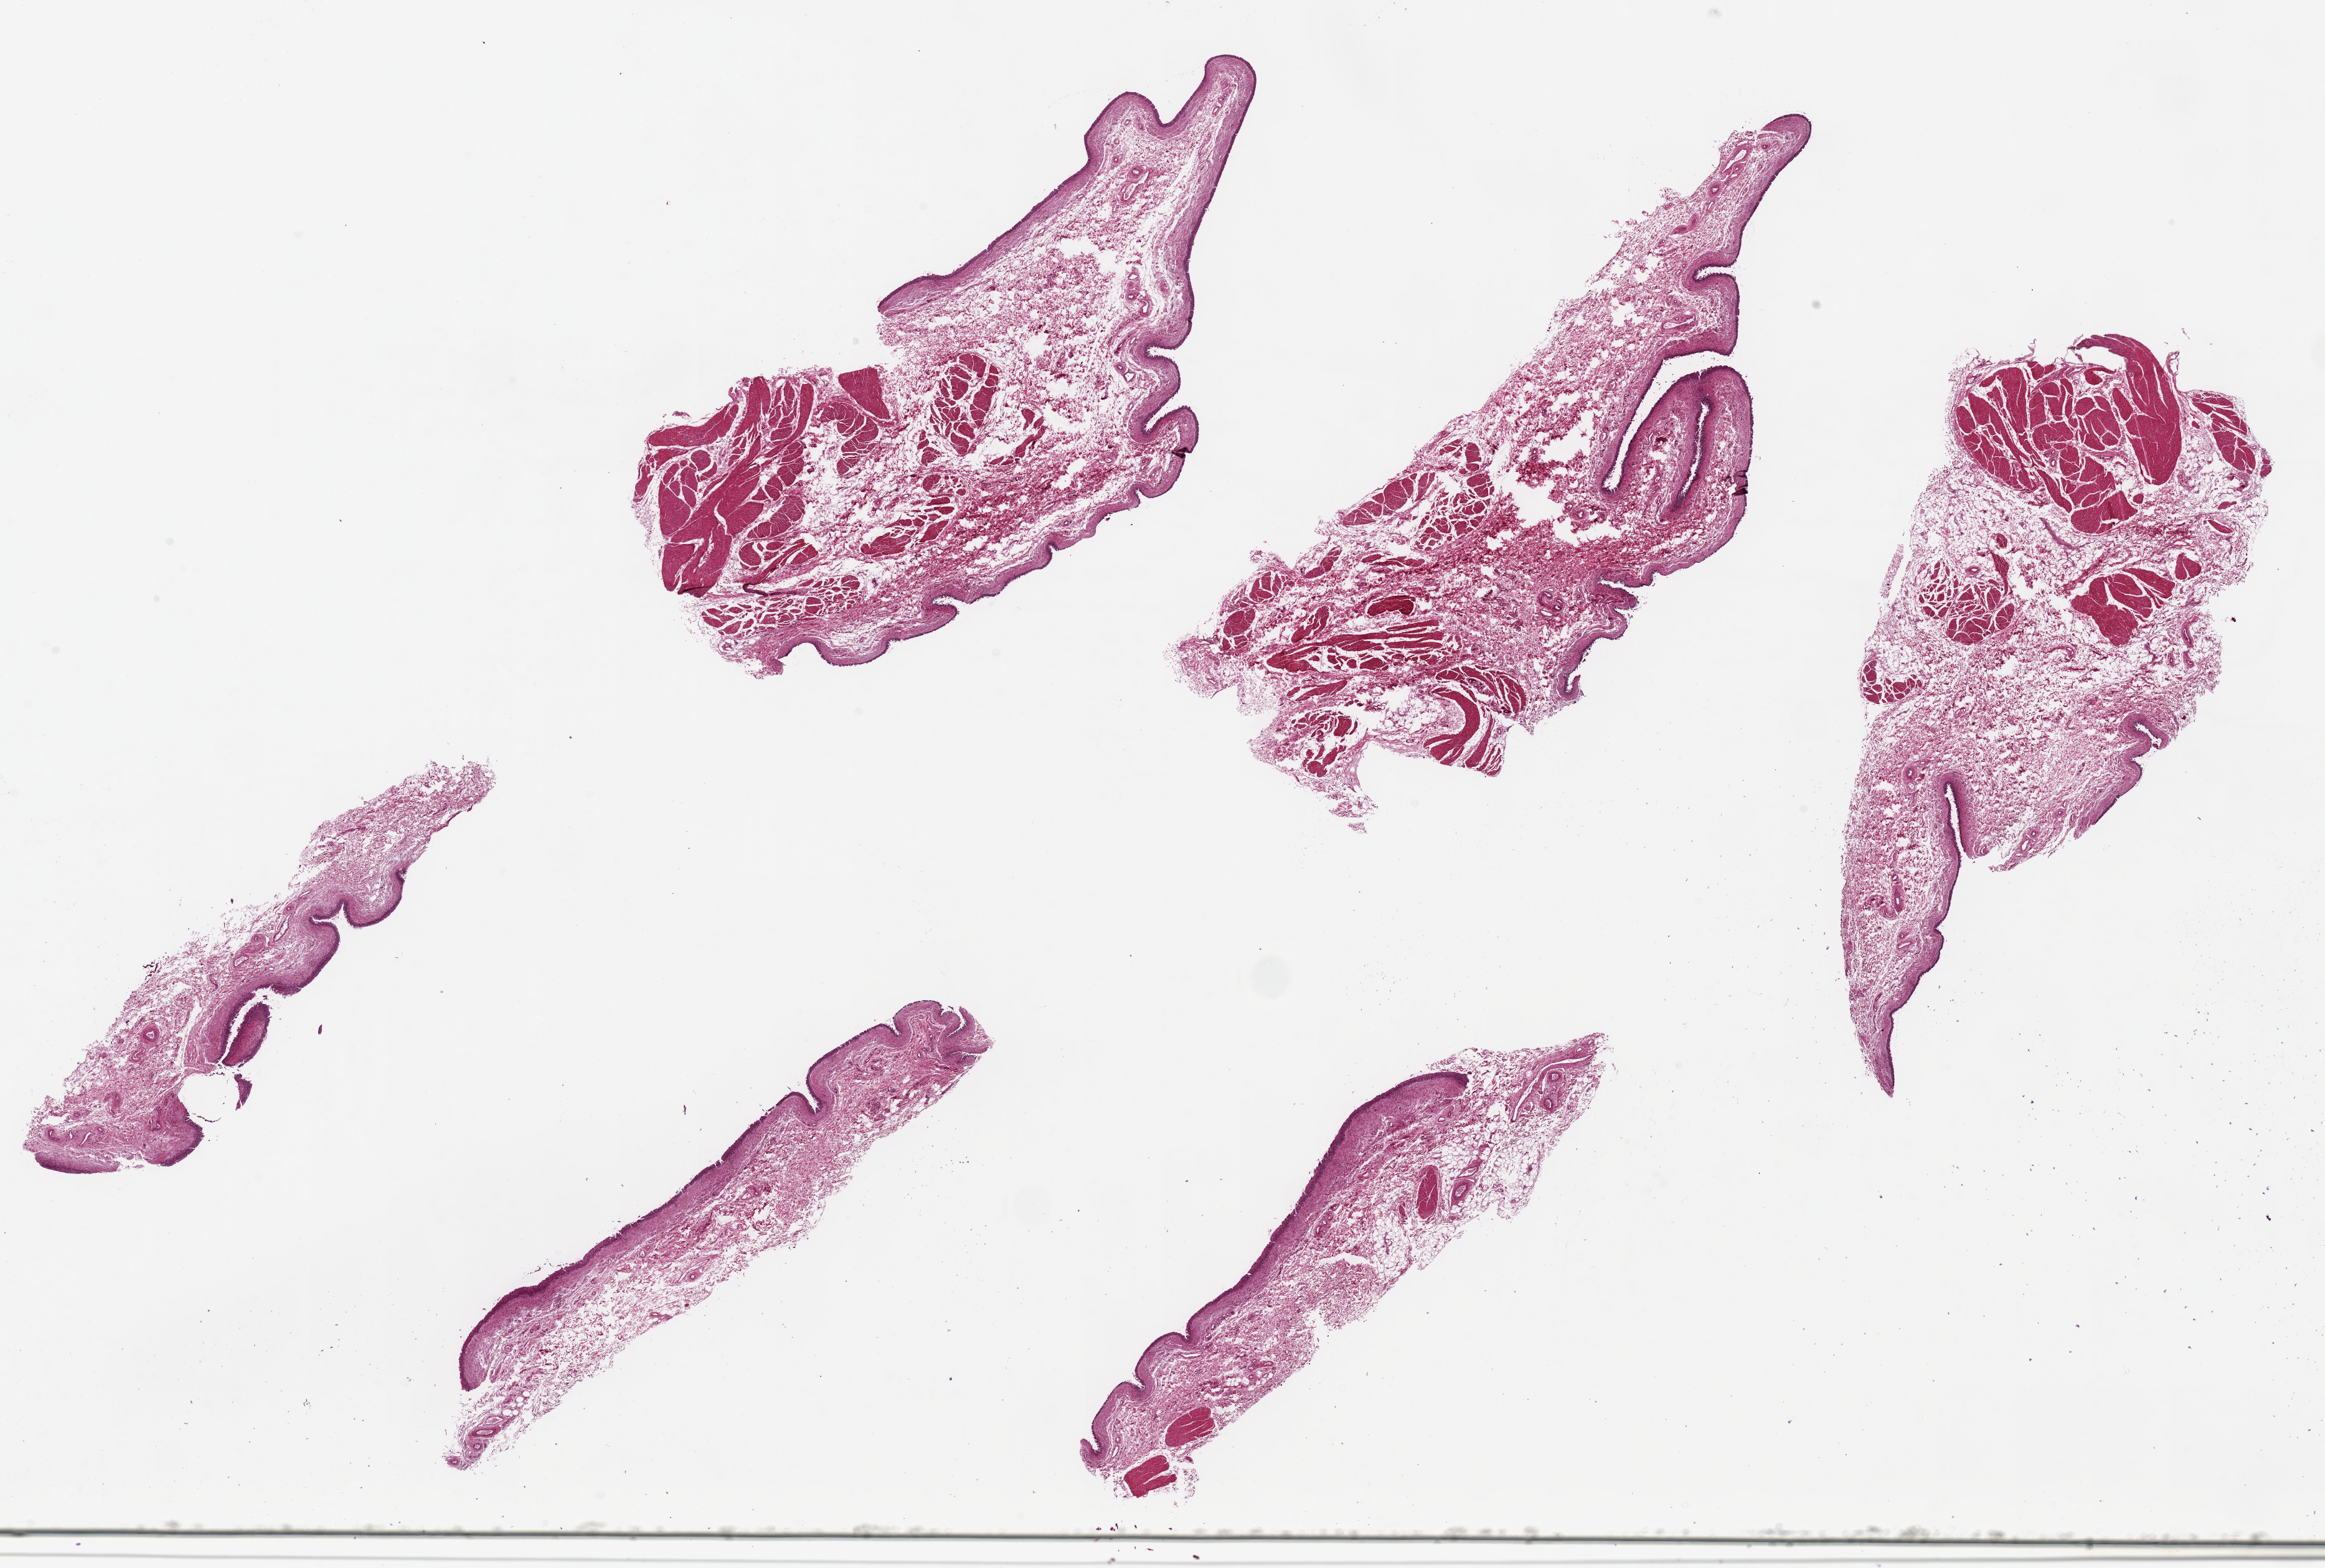
Whole-slide image, H&E stain — shown as a low-resolution overview of the whole scanned area (about 29.5 x 19.9 mm); PAXgene-fixed paraffin-embedded (PFPE) section; sampled site (target tissue): urinary bladder; donor tissue sample. Donor: male.
Review note (as recorded): 6 ~8.5x4mm pieces; Urothelium variably sloughed, <1% of thickness.